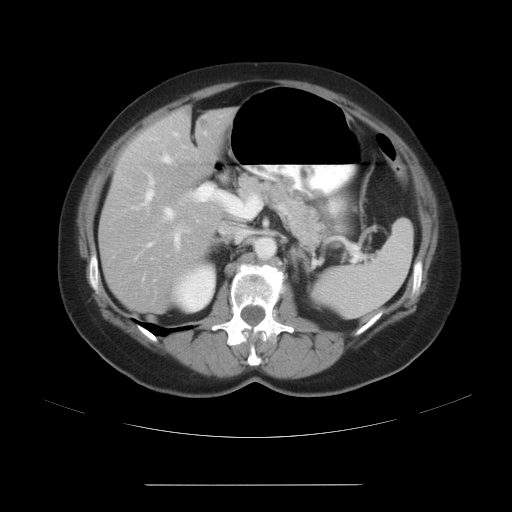
Contrast-enhanced abdominal CT, one axial slice. Position 16 of 27 along the scan axis. Reconstruction kernel STANDARD. 120 kVp. Soft-tissue window (W 400 / L 40 HU). 512 × 512 image matrix, field of view 440 × 440 mm. Female patient, age 58 years. From the clinical record (not read from this slice): diagnosis: colorectal cancer liver metastases, imaged before liver resection; multiple liver metastases: yes; largest metastasis: 1.9 cm.
Annotated regions visible in this slice (expert manual segmentation):
- hepatic veins: box from (x=161, y=154) to (x=199, y=223) px
- liver: (x=100, y=105)–(x=232, y=308)
- planned liver remnant (the part of the liver to remain after resection): (x=109, y=117)–(x=221, y=219)
- portal vein (with intrahepatic branches): (x=117, y=131)–(x=254, y=282)
- liver metastasis: (x=186, y=111)–(x=211, y=132)
- liver metastasis: (x=186, y=112)–(x=191, y=118)